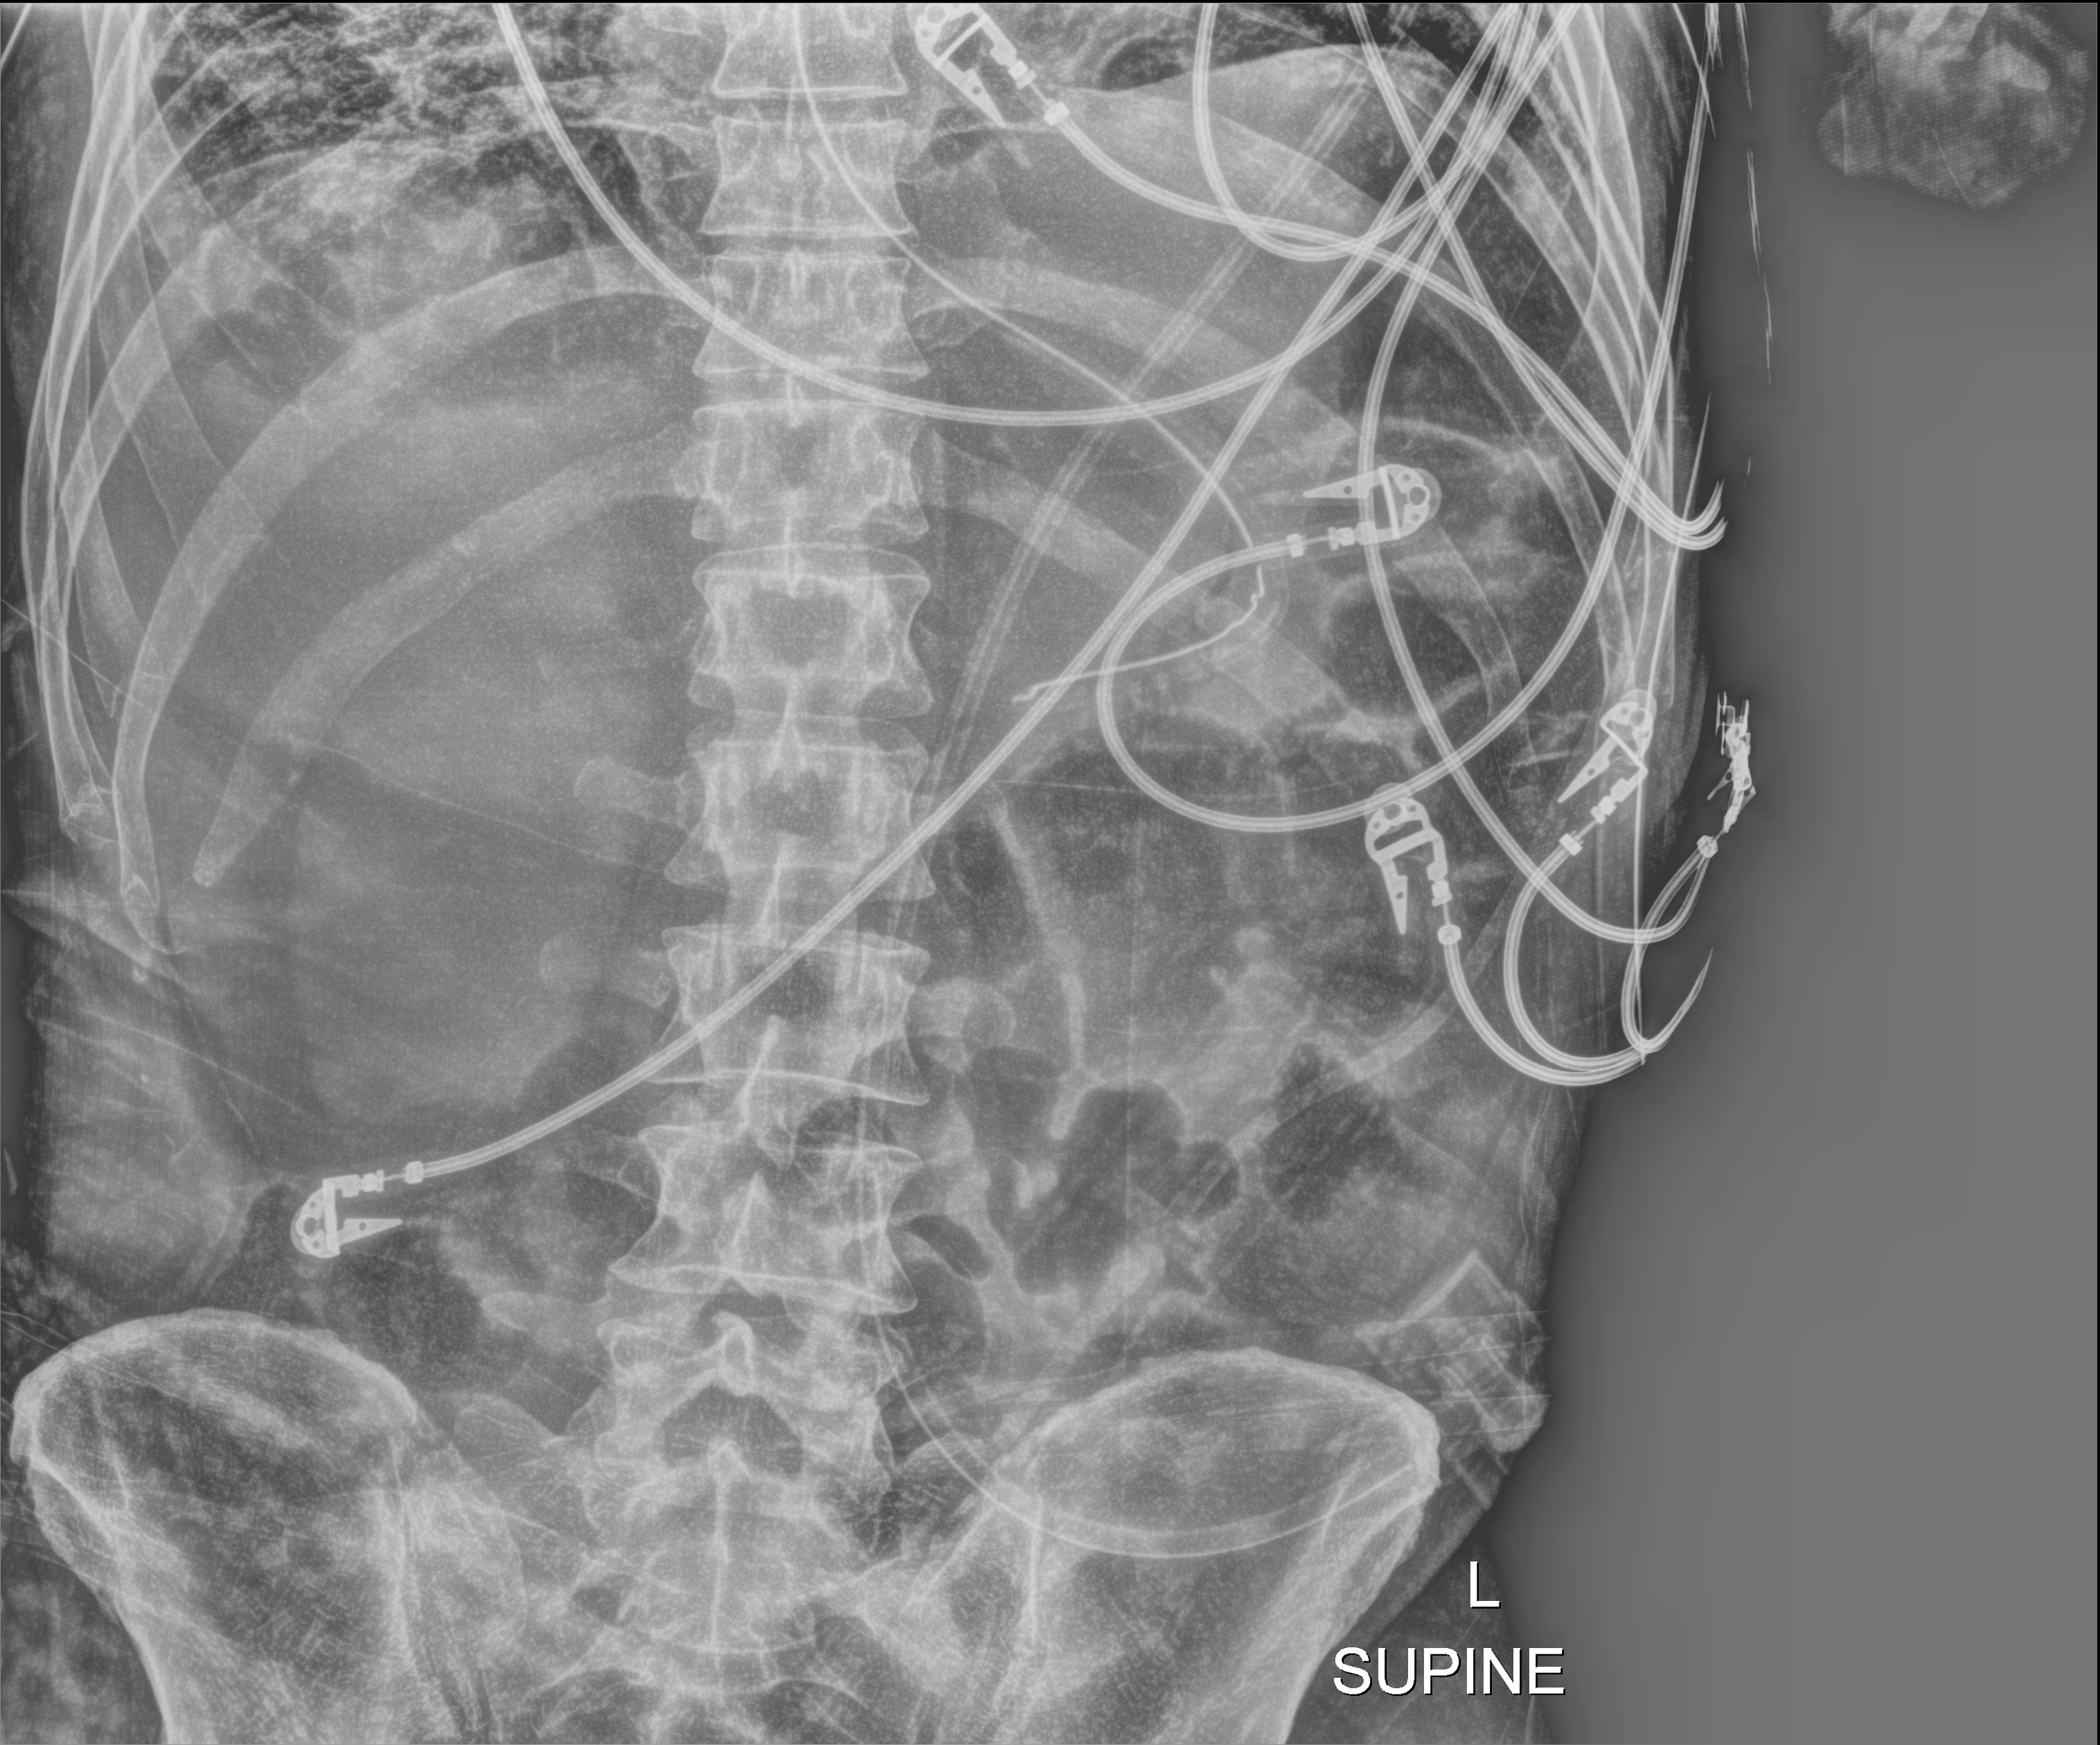
Portable abdomen radiograph, anteroposterior (AP) projection. Male patient hospitalised with COVID-19, age 18–59 years.
Admission-level facts for this patient (not findings on this image; timing relative to this image not recorded):
- other chronic lung disease (admission record): no